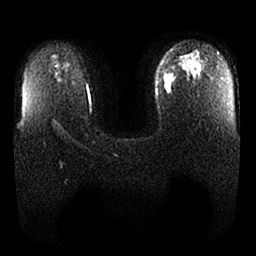
Breast MRI, one axial slice; slice 17 of 25 in the series (ordered by position); diffusion-weighted series; image 2 of 4 stored at this slice position (different b-values; order by instance number); 1.5 T; 4 mm slice thickness; 256 × 256 image matrix. Female patient.
Structures marked on this image (outlined manually by an expert reader):
- tumour on diffusion-weighted imaging: bounding box (x1, y1, x2, y2) in pixels: (162, 72, 176, 94)